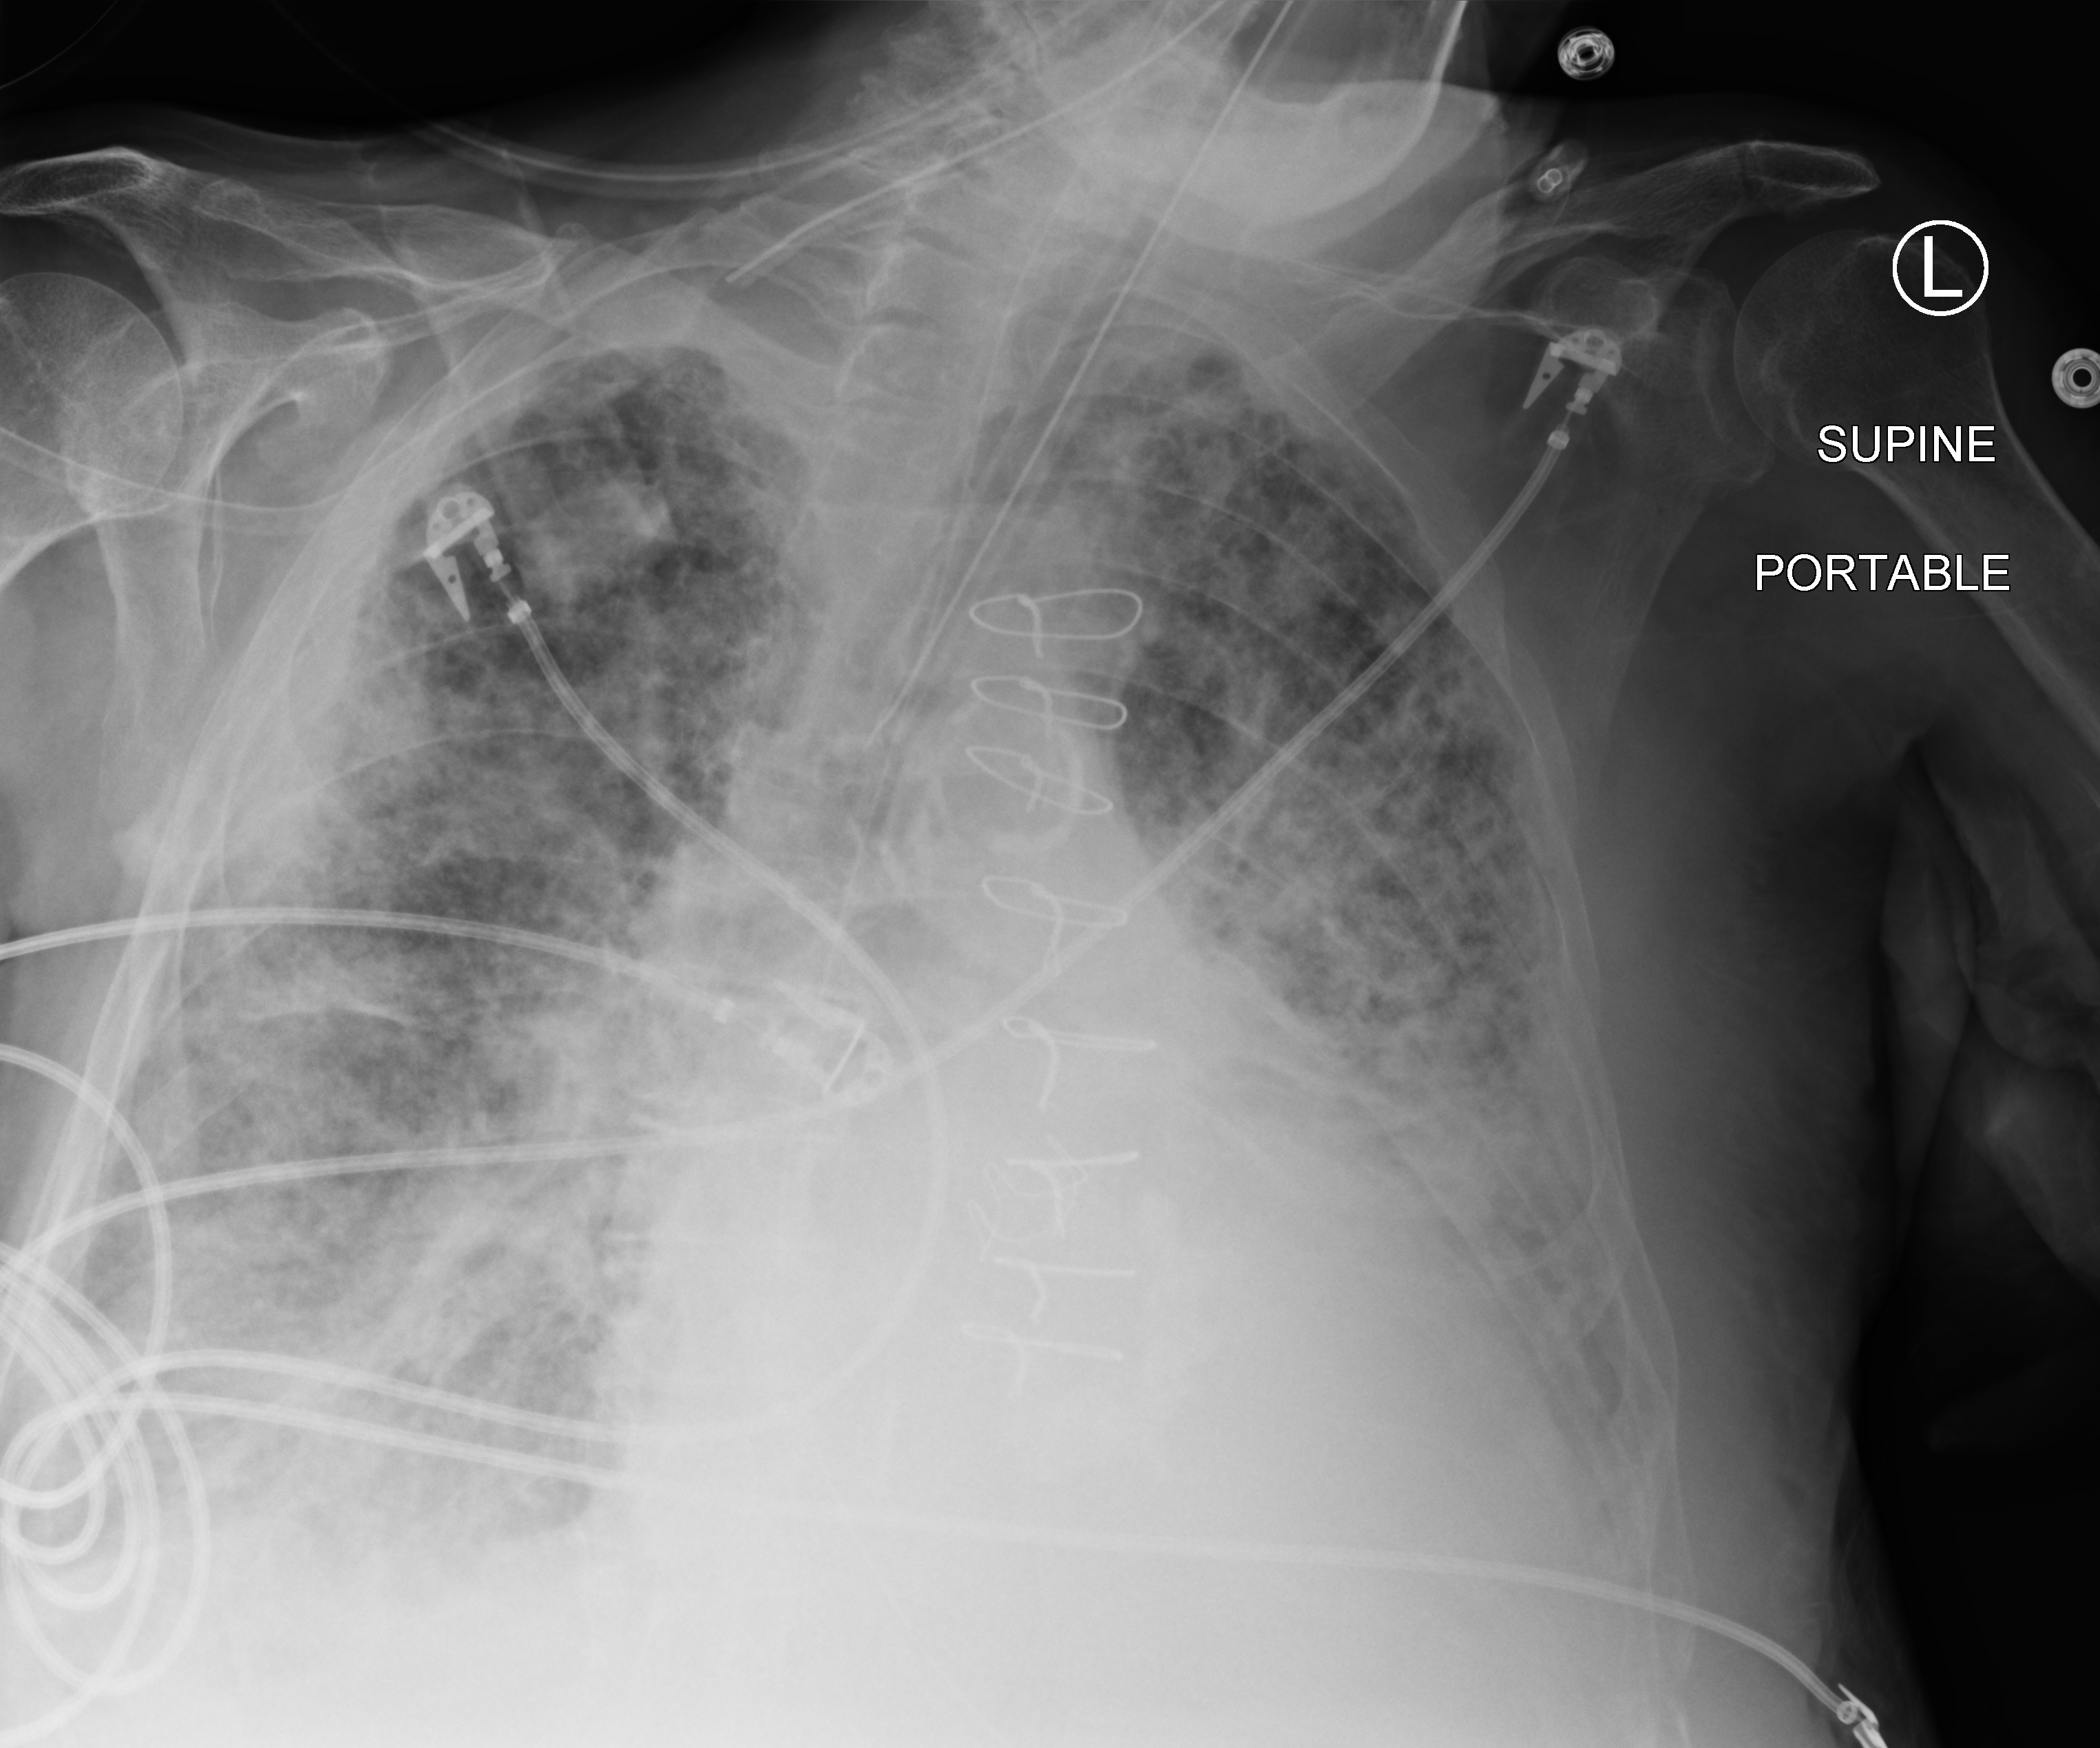
Bedside chest radiograph (computed radiography); anteroposterior (AP) projection. Patient hospitalised with COVID-19; male, aged 75–90 years.
From the hospital-stay record, not from the radiograph (when in the stay this image was taken is not recorded): admitted to intensive care during this hospital stay: yes.